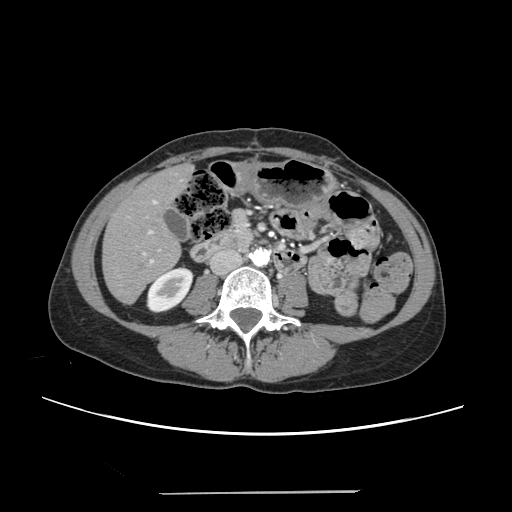
Contrast-enhanced abdominal CT, one axial slice; 120 kVp; intravenous contrast given; soft-tissue window (W 400 / L 40 HU); 512 × 512 image matrix, field of view 371 × 371 mm. Female patient, age 60 years. From the clinical record (not read from this slice): diagnosis: colorectal cancer liver metastases, imaged before liver resection; multiple liver metastases: no; largest metastasis: 1.5 cm; disease in both lobes: no.
Structures marked on this image (expert manual segmentation):
- liver: bounding box (x1, y1, x2, y2) in pixels: (104, 166, 191, 302)
- planned liver remnant (the part of the liver to remain after resection): (104, 172, 180, 302)
- portal vein (with intrahepatic branches): (142, 200, 160, 263)